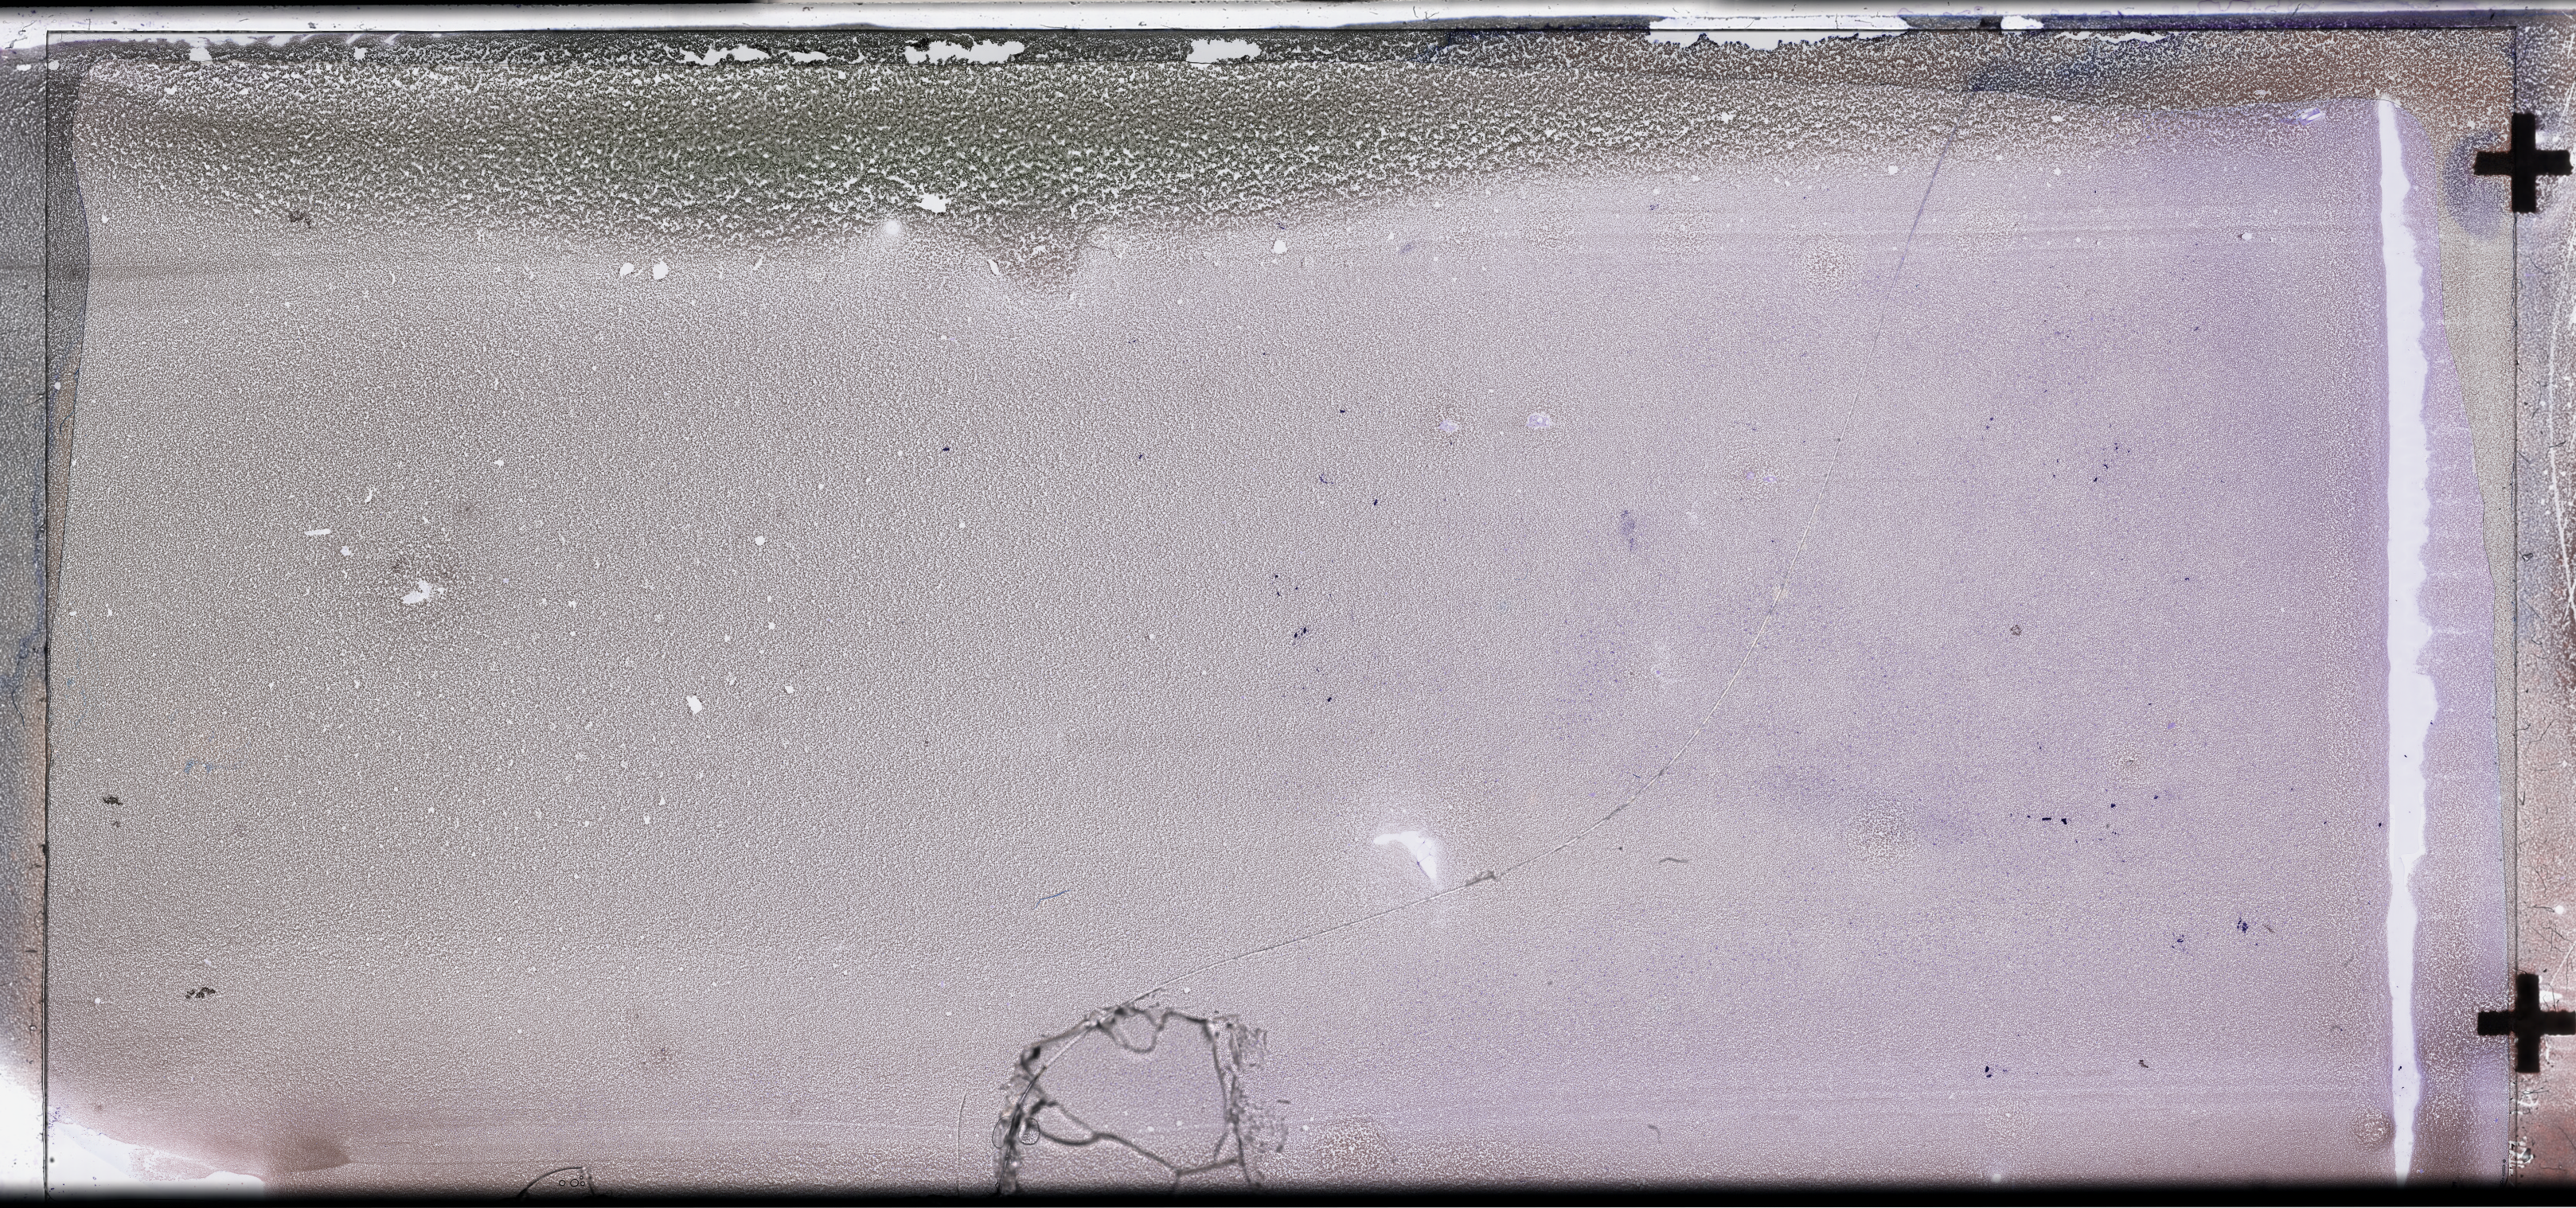
Whole-slide image of a bone marrow smear, Wright–Giemsa stain — low-resolution overview of the scanned area, about 52.3 x 24.5 mm; EDTA-anticoagulated smear; specimen time point: collected at disease progression. Patient: female.
• from a patient with: Acute Myeloid Leukemia Not Otherwise Specified